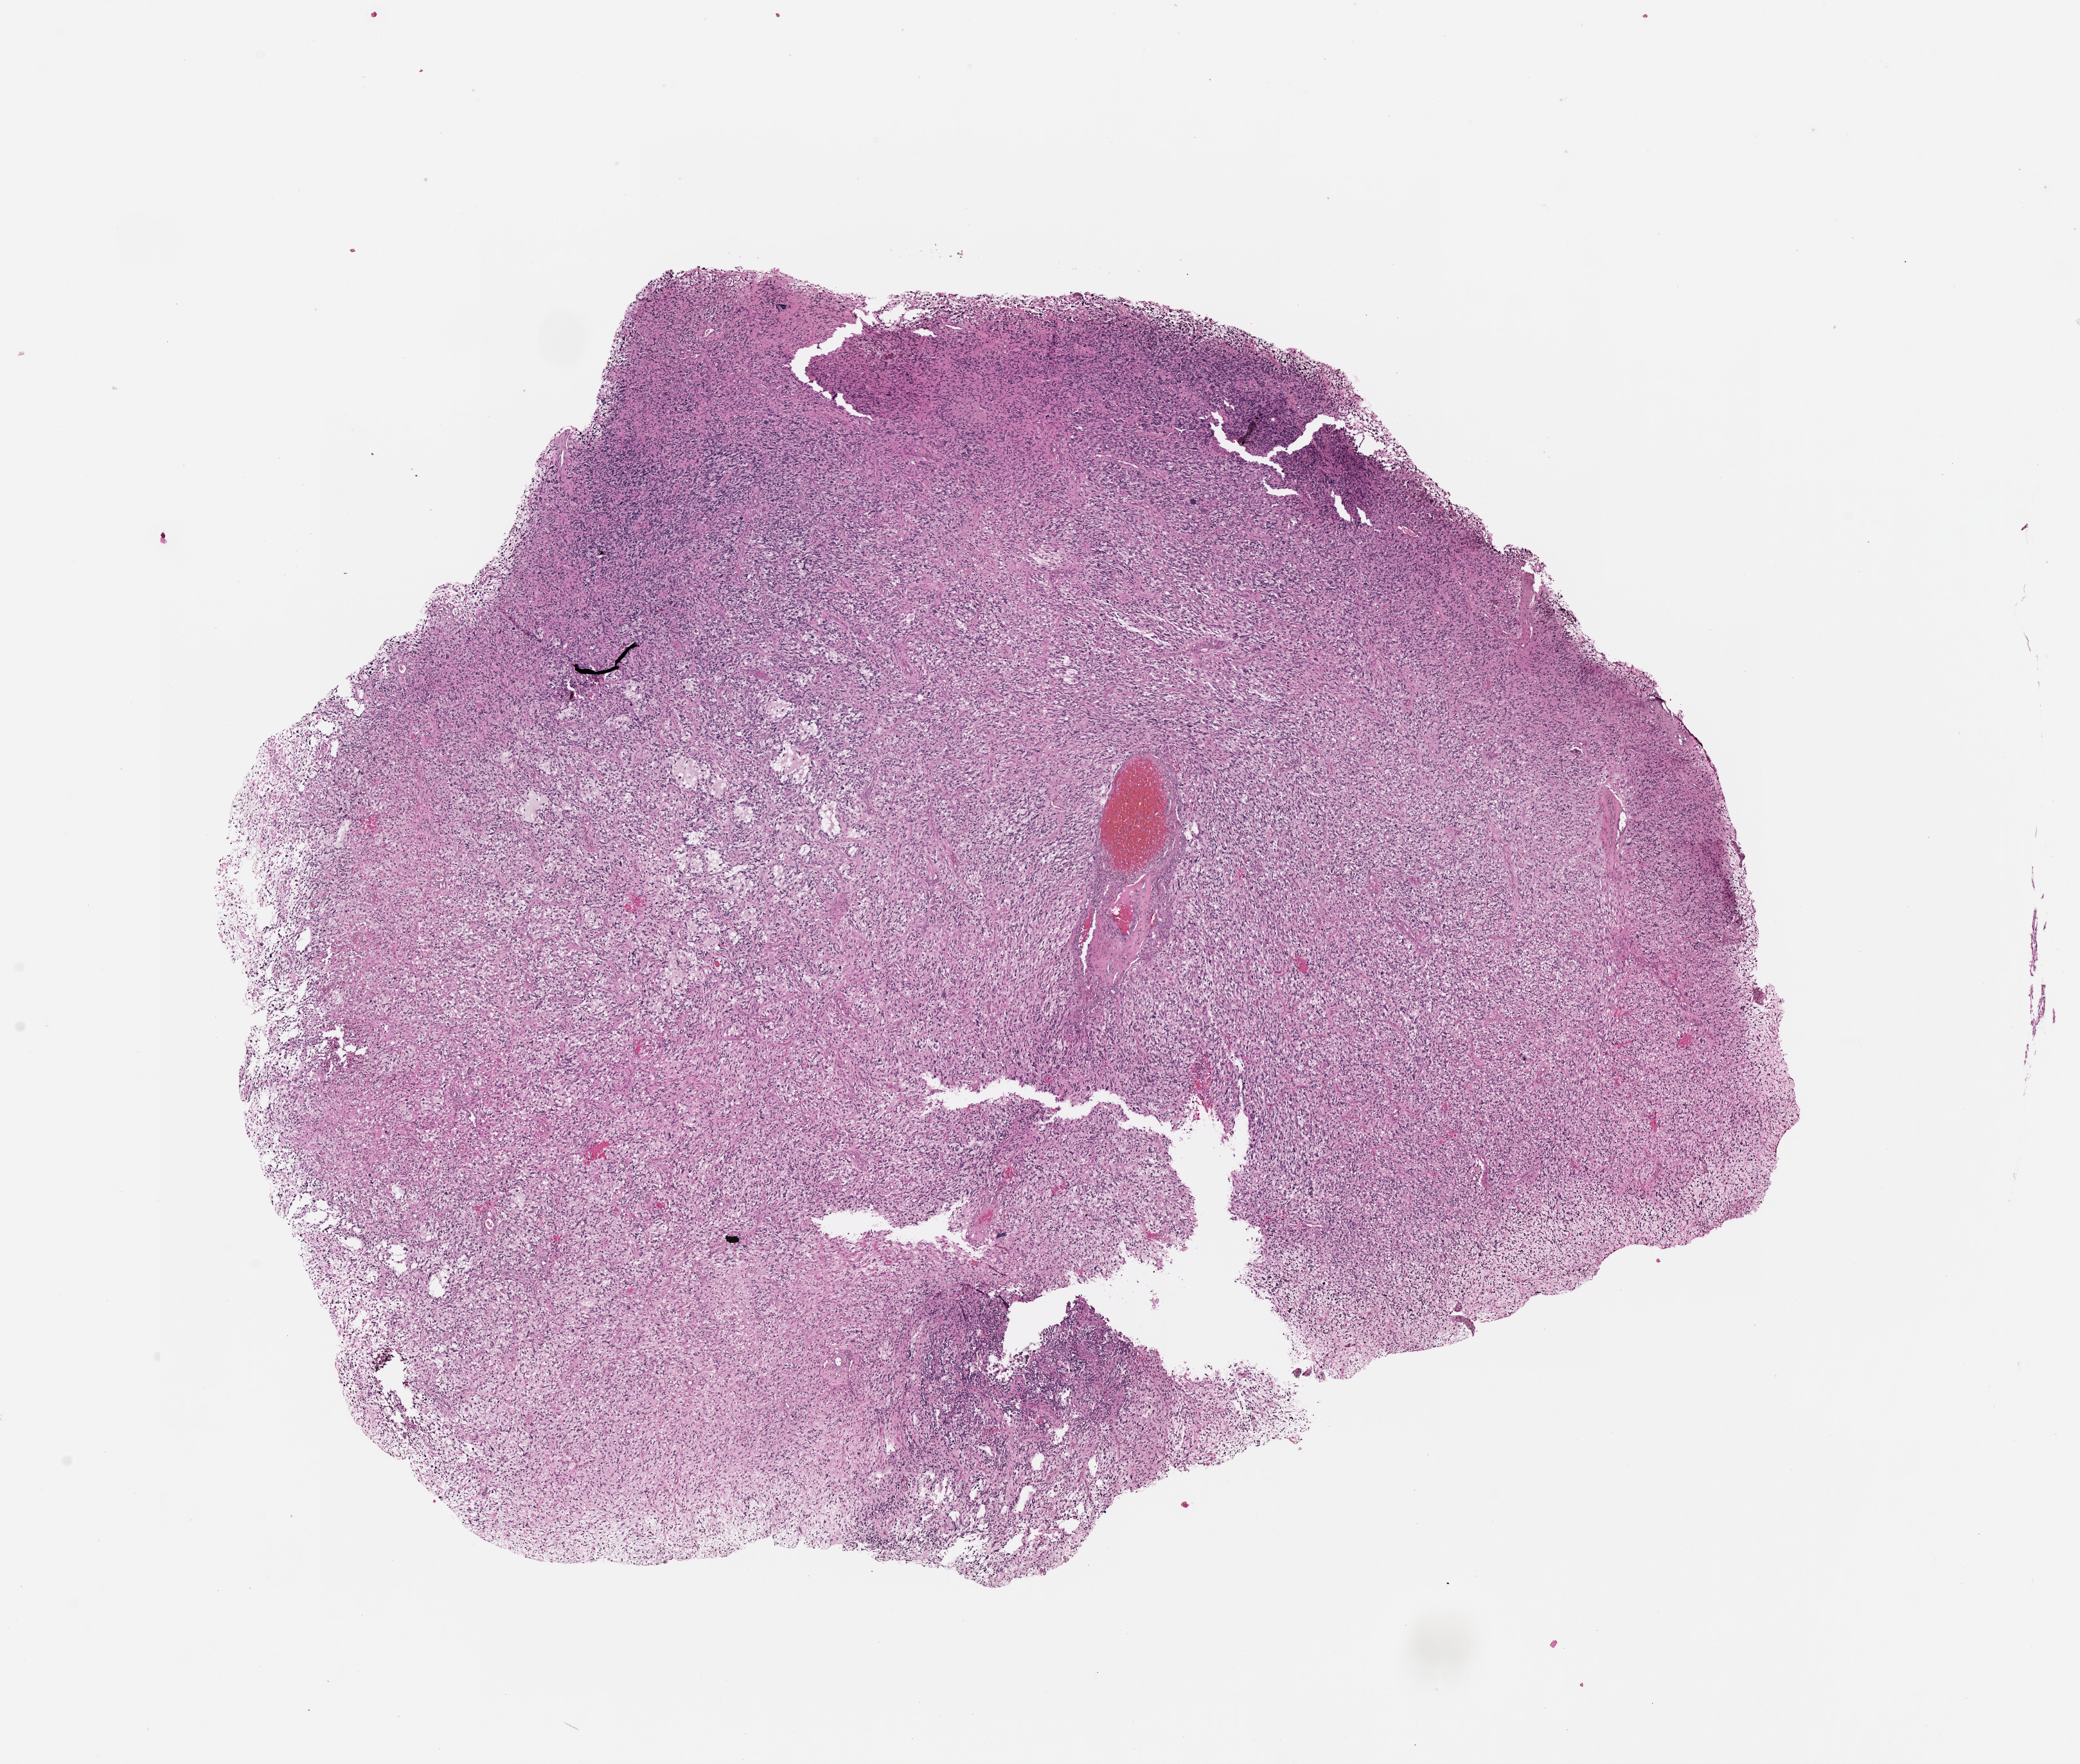
Hematoxylin and eosin (H&E) stained whole-slide image, shown as a low-resolution overview of the whole scanned area (about 13.0 x 11.0 mm). Tumour tissue sample, sampled site: frontal lobe. Male, 31 y/o. Pathologist review of this section (percent, as recorded): tumour nuclei 70%, necrosis 10%.
Diagnosis: Glioblastoma. Primary tumour site (as recorded): frontal lobe.